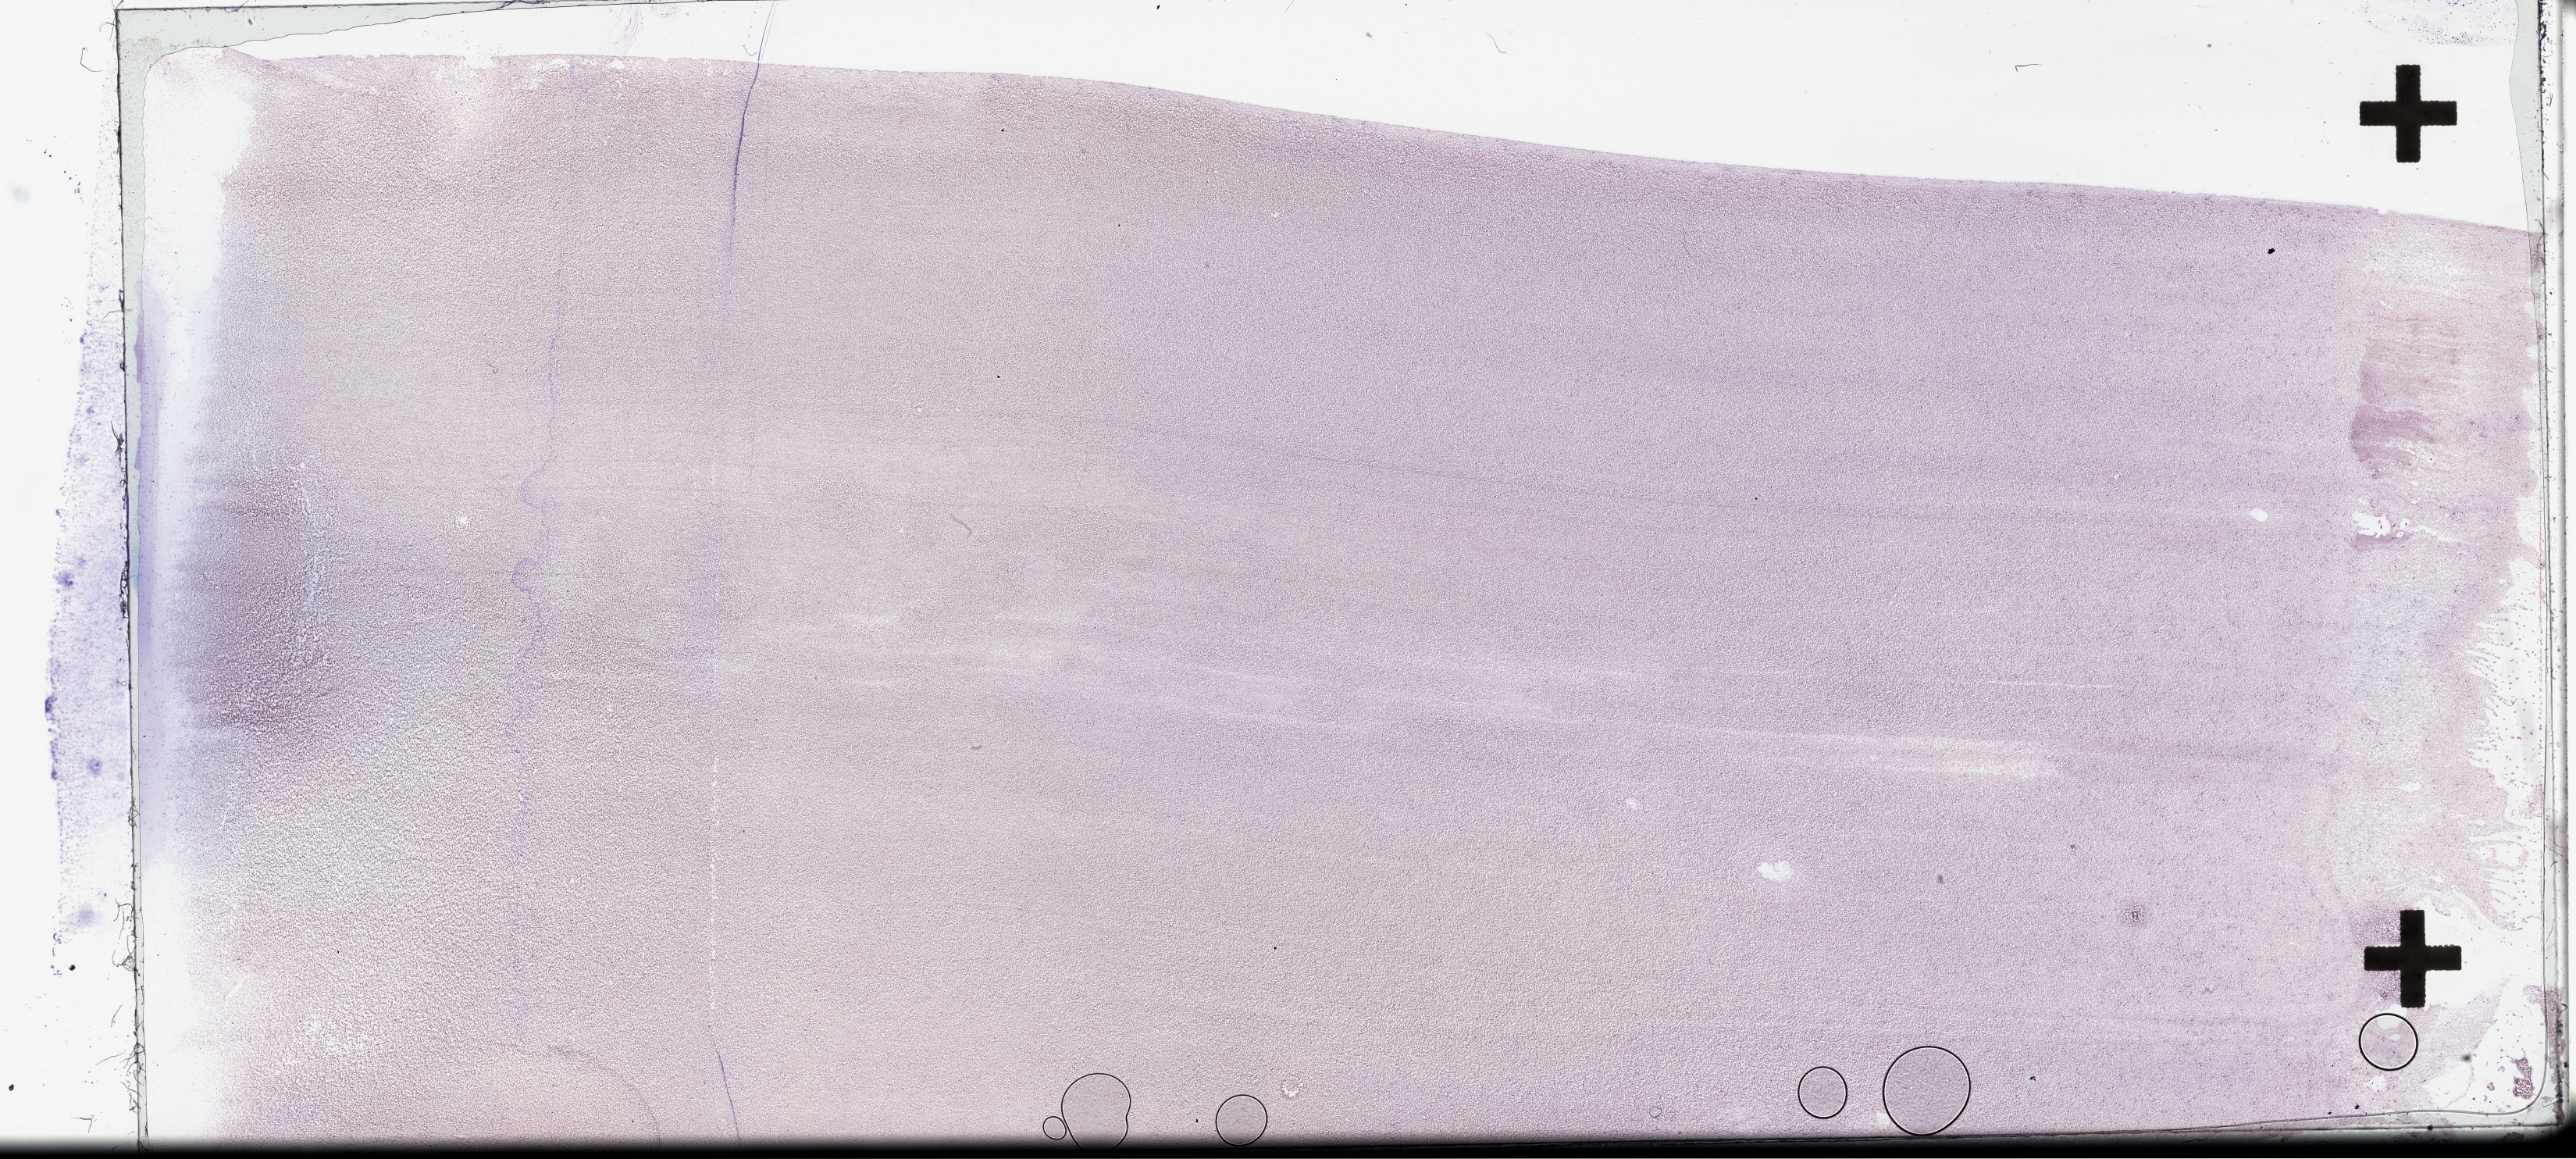
Digitized H&E-stained tissue section (whole slide), shown as a low-resolution overview of the whole scanned area (about 53.3 x 24.0 mm); peripheral blood (leukaemic) sample. Female, 57 y/o.
Diagnosis: Acute Myeloid Leukemia. FAB classification: M2.